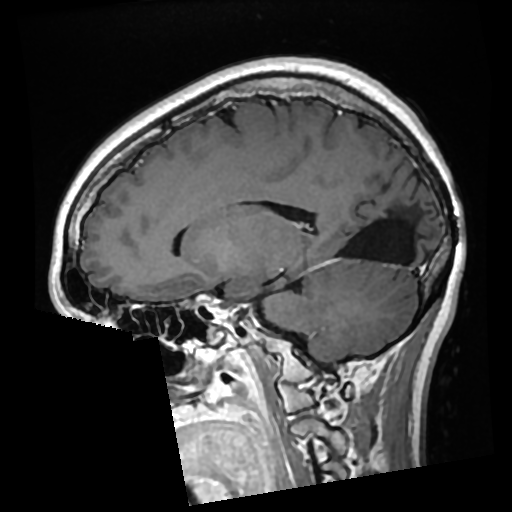
Brain MRI from a brain-tumour surgery series, one sagittal slice; position 117 of 276 along the scan axis; T1-weighted post-contrast; 512 × 512 image matrix. Case-level facts recorded for this patient, not image findings: histopathology: Glioma with ependymal features; WHO grade: 2; tumour location: Left Parietal.
Structures marked on this image (expert manual segmentation):
- previous resection cavity: bounding box (x1, y1, x2, y2) in pixels: (340, 196, 420, 262)